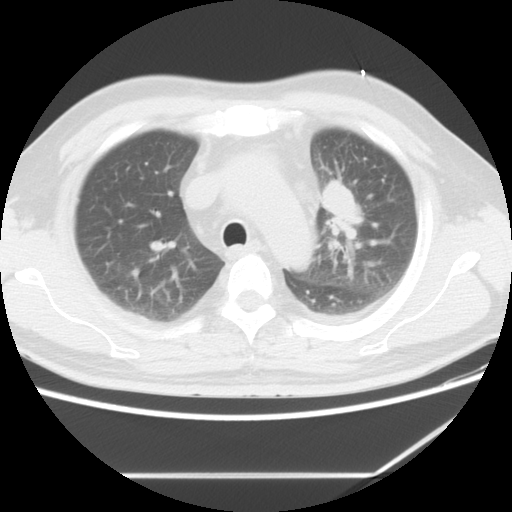
Chest CT, one axial slice; slice 6 of 13 in the series (ordered by position); 120 kVp; lung window (W 1500 / L -600 HU); 5 mm slice thickness; 512 × 512 image matrix, field of view 350 × 350 mm. Patient: male, 56 years. Case-level facts recorded for this patient, not image findings: clinical TNM (as recorded): T2 N3 M1.
Structures marked on this image (bounding box drawn by a radiologist):
- lung tumour (recorded histology: adenocarcinoma): bounding box <313,172,367,244> (left, top, right, bottom; pixels)